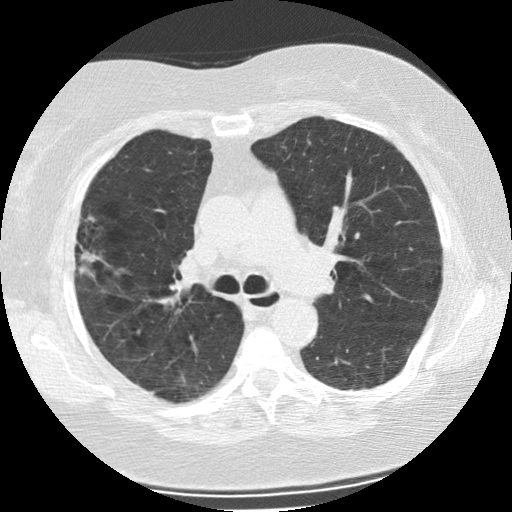
Low-dose screening chest CT, one axial slice; slice 147 of 225 in the series (ordered by position); 120 kVp; lung window (W 1500 / L -600 HU); 2.5 mm slice thickness; 512 × 512 image matrix, field of view 320 × 320 mm.
Outlined on this slice (manually delineated by an expert):
- lesion 1 (tumor, upper lobe of right lung): bounding box <79,251,99,276> (left, top, right, bottom; pixels)